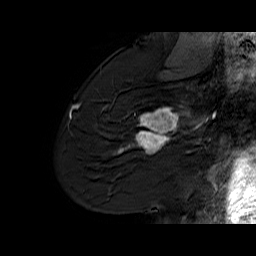
Breast MRI (dynamic contrast-enhanced), one sagittal slice; position 42 of 60 along the scan axis; dynamic contrast-enhanced series, time point 2 of 6 at this slice position (early post-contrast); 1.5 T; TE 6.1 ms, TR 32.9 ms; 4 mm slice thickness; 256 × 256 image matrix, field of view 220 × 220 mm. Female patient. Case-level facts recorded for this patient, not image findings: setting: breast cancer imaged before/during neoadjuvant chemotherapy; receptor status: HER2-positive.
Structures marked on this image (semi-automatic segmentation, software-assisted and operator-edited):
- analysis volume of interest (the breast-tissue region the enhancement analysis was run in; not a lesion): bounding box (x1, y1, x2, y2) in pixels: (127, 96, 194, 165)
- tumour enhancement mask (voxels above the 100 % enhancement threshold inside the analysis volume of interest): (127, 108, 194, 153)